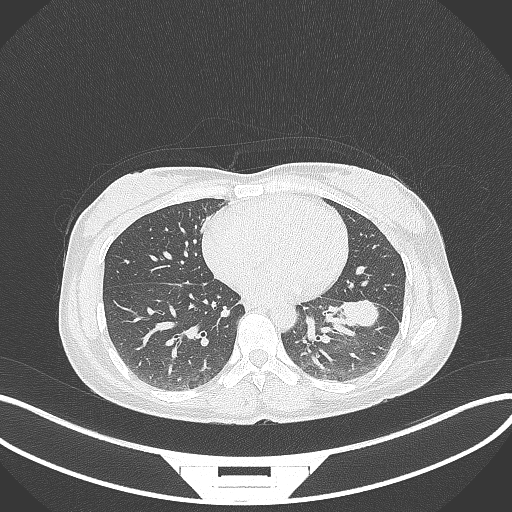
Chest CT, one axial slice; position 29 of 244 along the scan axis; 120 kVp; lung window (W 1500 / L -600 HU); 1 mm slice thickness; 512 × 512 image matrix, field of view 400 × 400 mm. Female patient, age 41 years. From the clinical record (not read from this slice): clinical TNM (as recorded): T2a N3 M1b.
Outlined on this slice (bounding box drawn by a radiologist):
- lung tumour (recorded histology: adenocarcinoma): bounding box <340,296,381,332> (left, top, right, bottom; pixels)